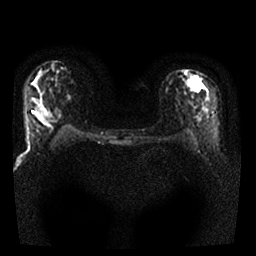
Breast MRI, one axial slice; position 13 of 25 along the scan axis; diffusion-weighted series; image 2 of 4 stored at this slice position (different b-values; order by instance number); 1.5 T; 256 × 256 image matrix. Female patient.
Annotated regions visible in this slice (expert manual segmentation):
- tumour on diffusion-weighted imaging: bounding box (x1, y1, x2, y2) in pixels: (188, 77, 203, 92)